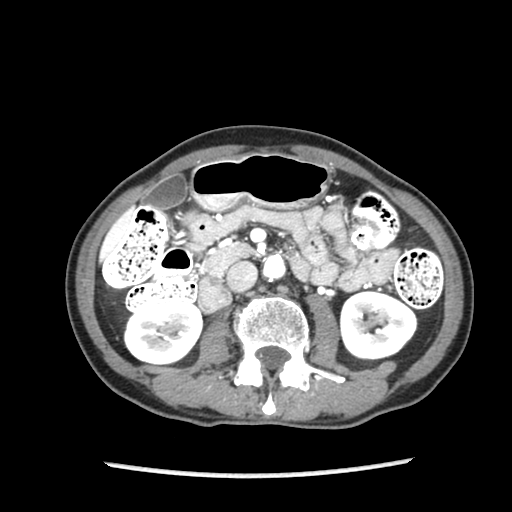
Contrast-enhanced abdominal CT (liver protocol), one axial slice. Slice 33 of 87 in the series (ordered by position). Soft-tissue window (W 400 / L 40 HU). 512 × 512 image matrix, field of view 300 × 300 mm. Case-level facts recorded for this patient, not image findings: diagnosis: hepatocellular carcinoma (patient treated with transarterial chemoembolisation; whether this scan precedes or follows treatment is not stated here); TNM stage (as recorded): Stage-IIIB; Child-Pugh class: A; tumour differentiation: well differentiated.
Annotated regions visible in this slice (semi-automatically segmented with operator editing):
- liver parenchyma outside the tumour (the mass and vessels are separate outlines, so this box may not span the whole liver): bounding box [x1, y1, x2, y2] px = [117, 209, 132, 222]